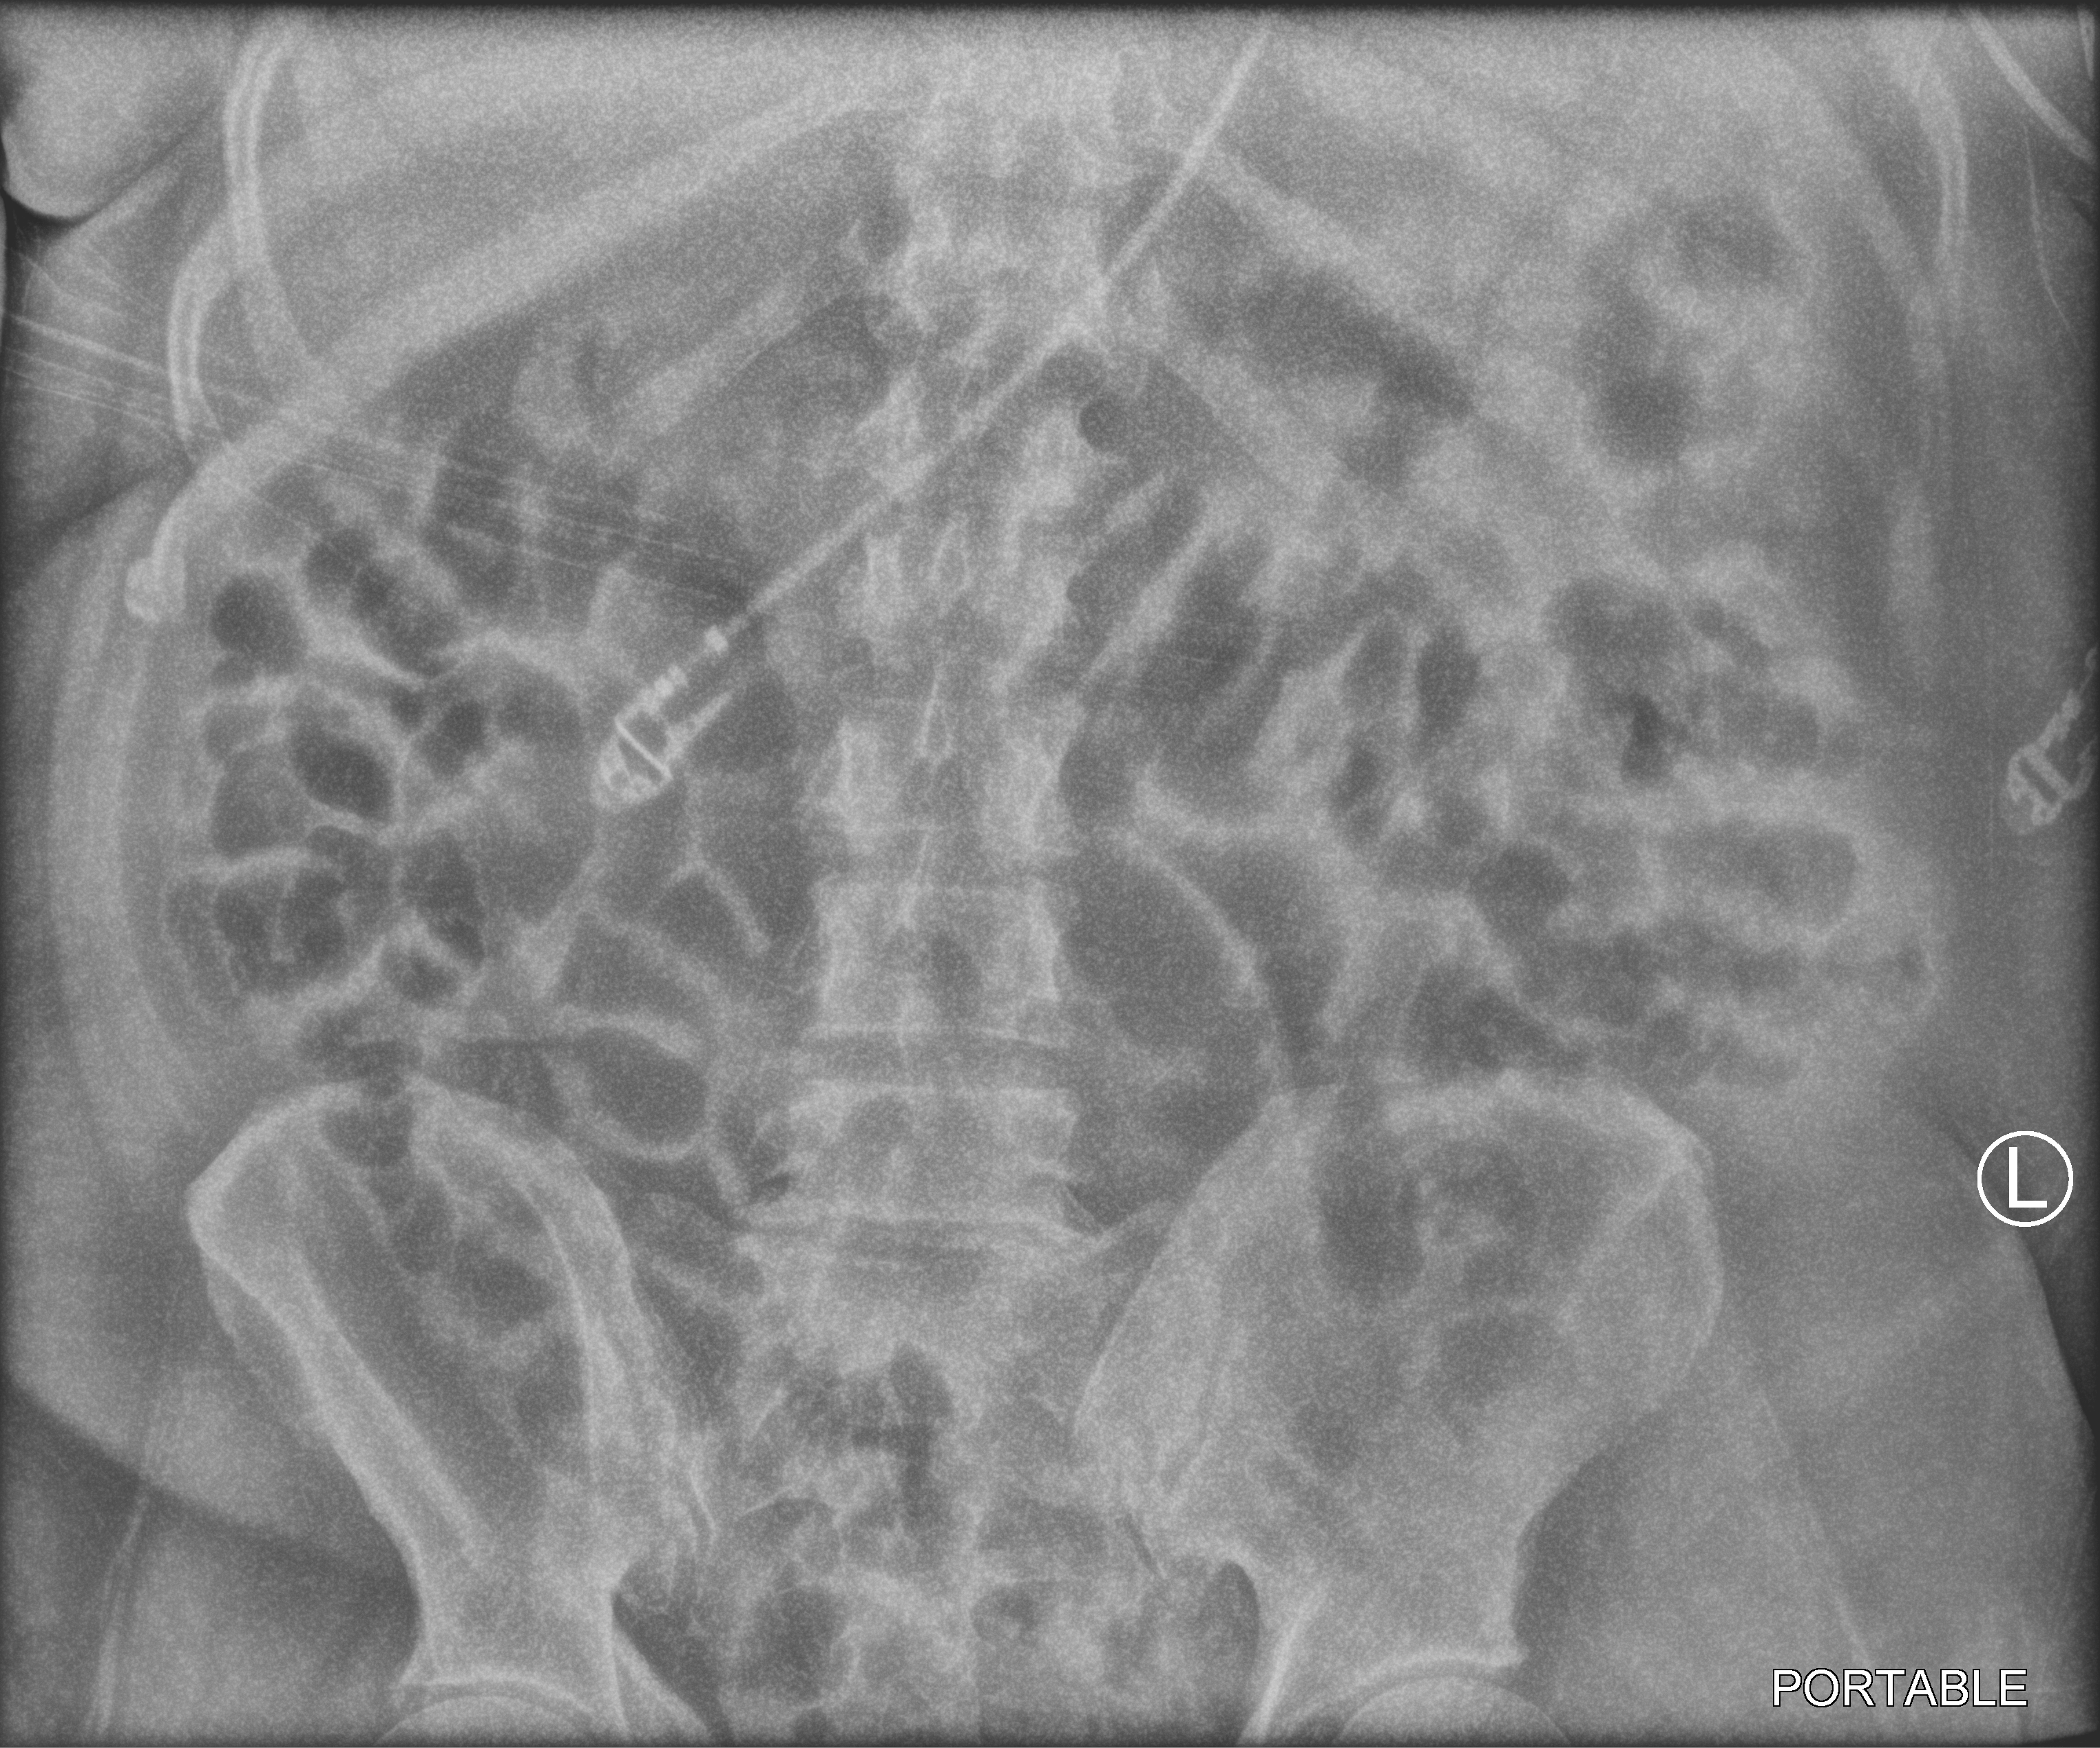
Abdomen X-ray; anteroposterior (AP) projection. Male patient hospitalised with COVID-19, age 60–74 years.
Admission-level facts for this patient (not findings on this image; timing relative to this image not recorded): diabetes (admission record): no; admitted to intensive care during this hospital stay: yes.